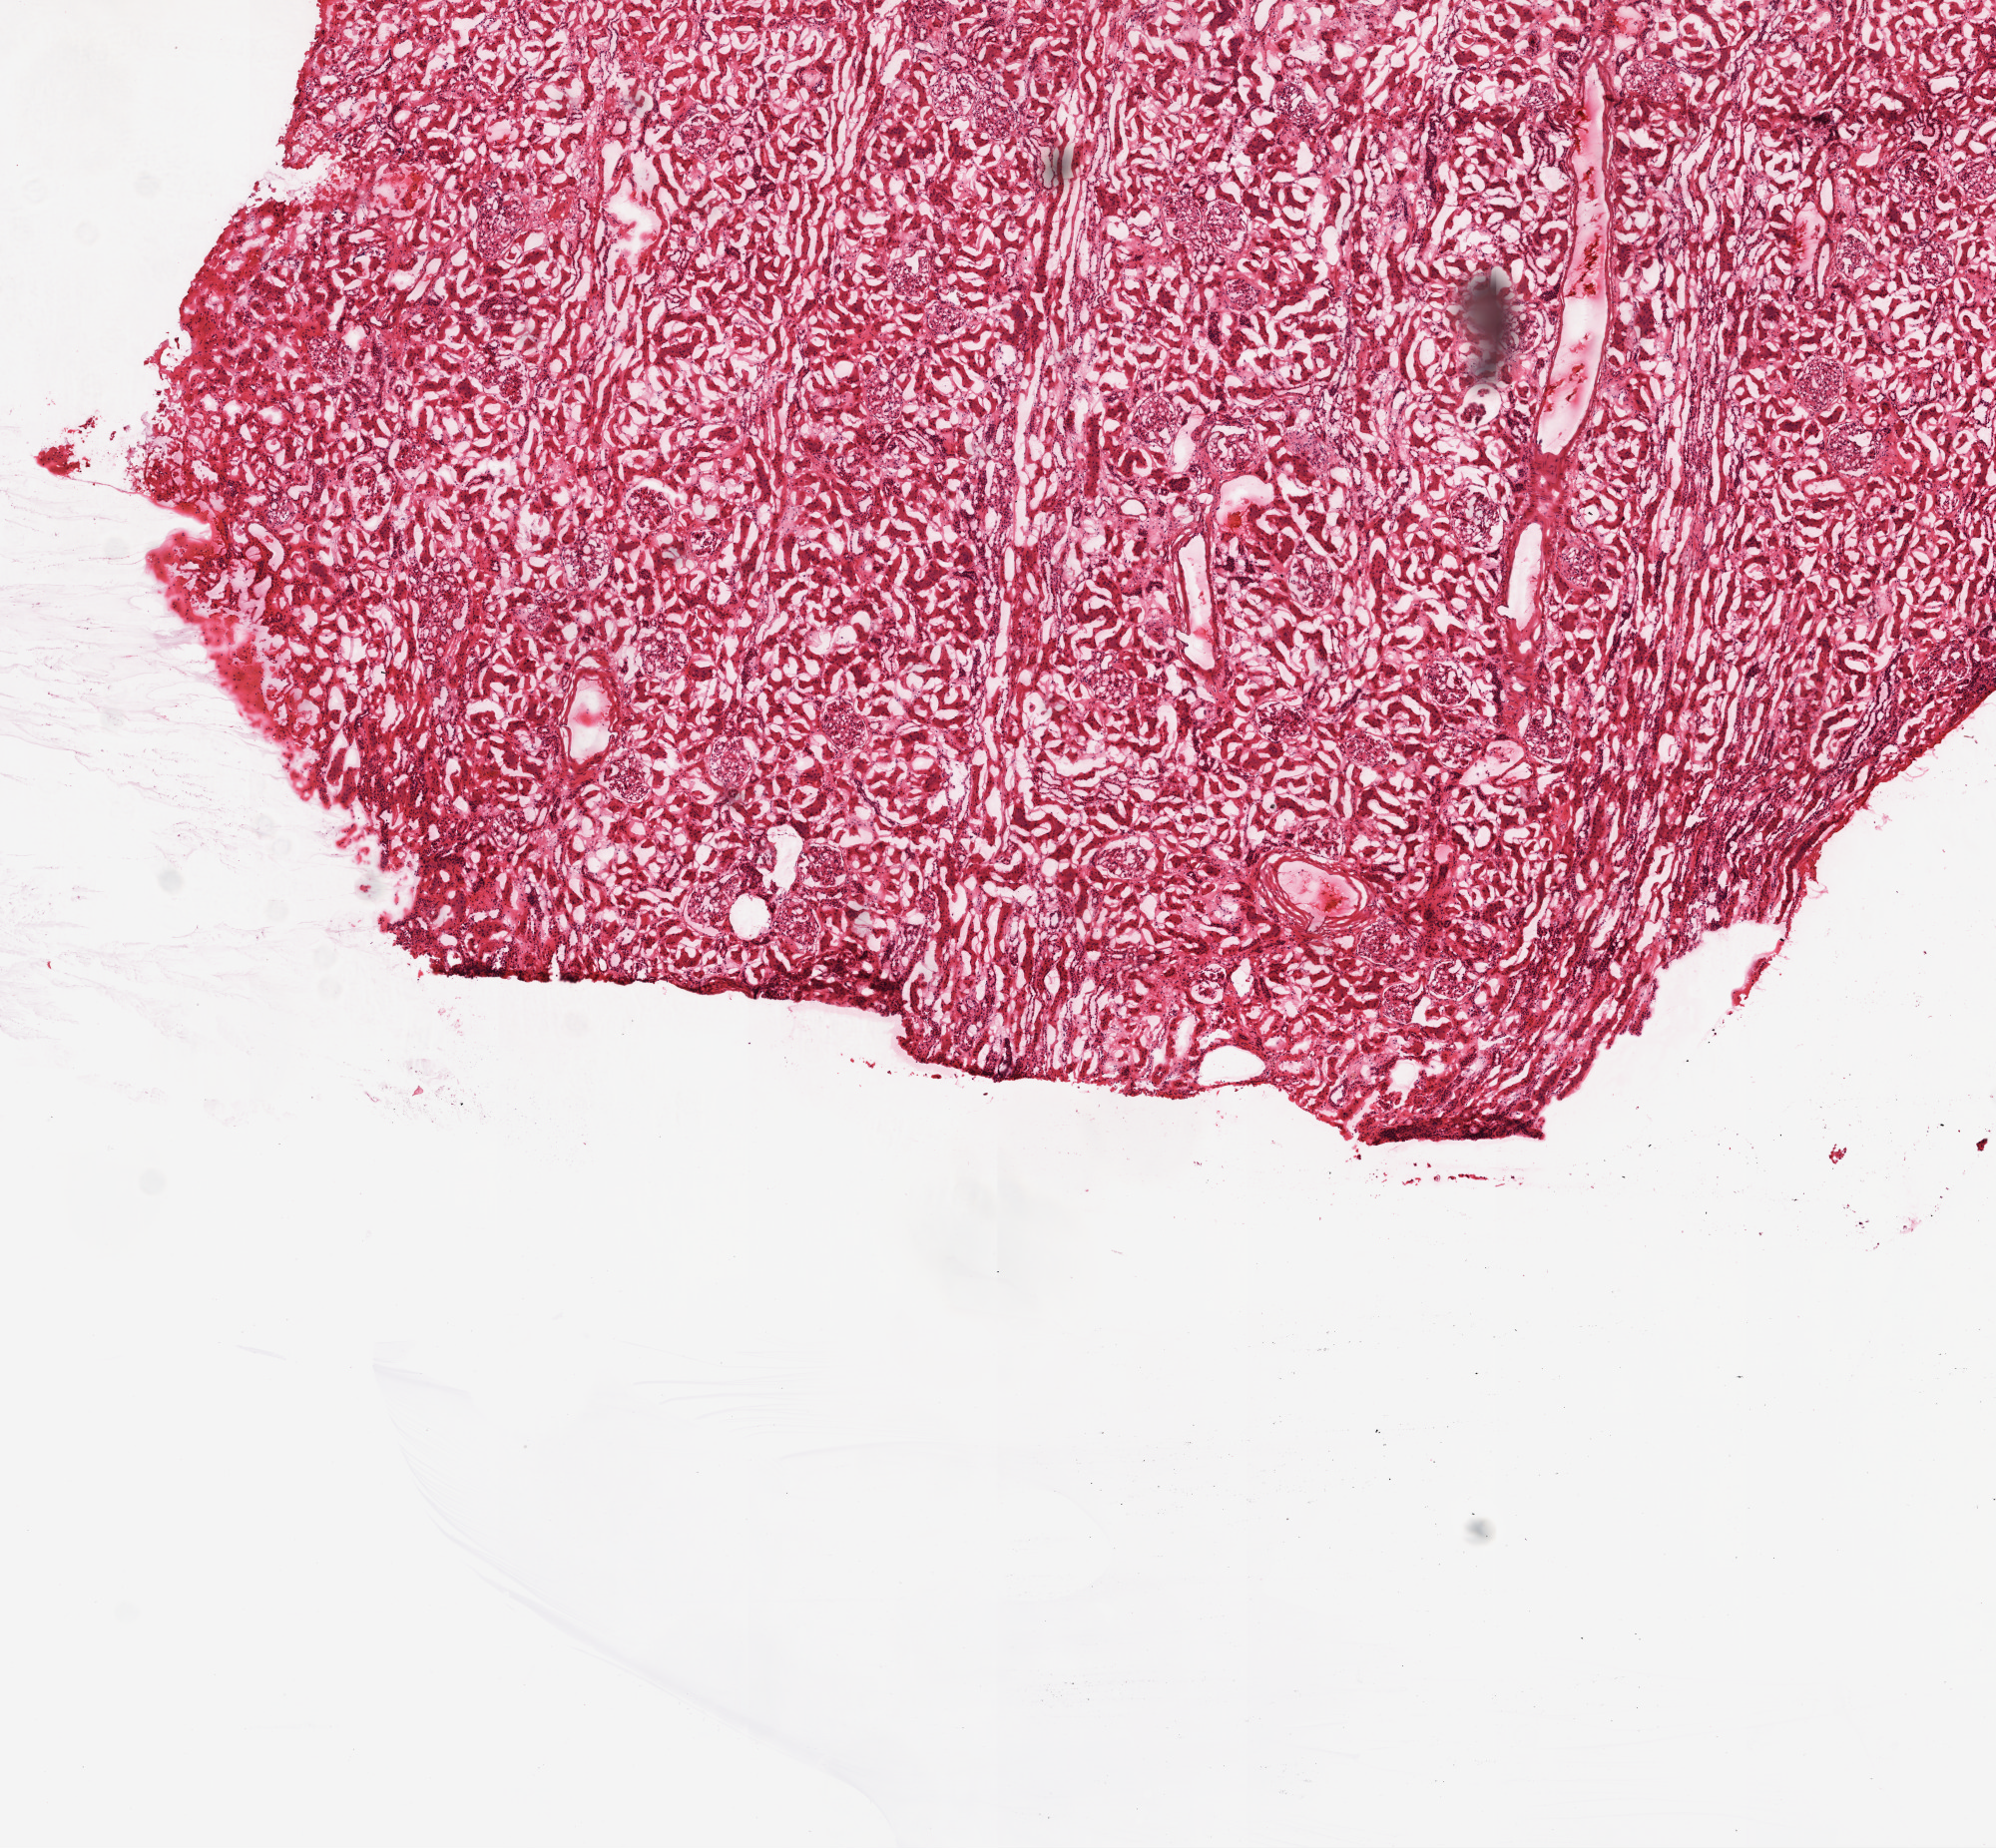
Whole-slide histology image, H&E — a low-resolution overview of the entire scanned area, about 8.0 x 7.4 mm; frozen section from the top of the tissue portion; sample: solid tissue normal (non-tumour tissue), kidney. Female, age 72 years at initial diagnosis.
• this section: solid tissue normal (non-tumour) sample from the same patient
• patient diagnosis: Clear cell adenocarcinoma, NOS